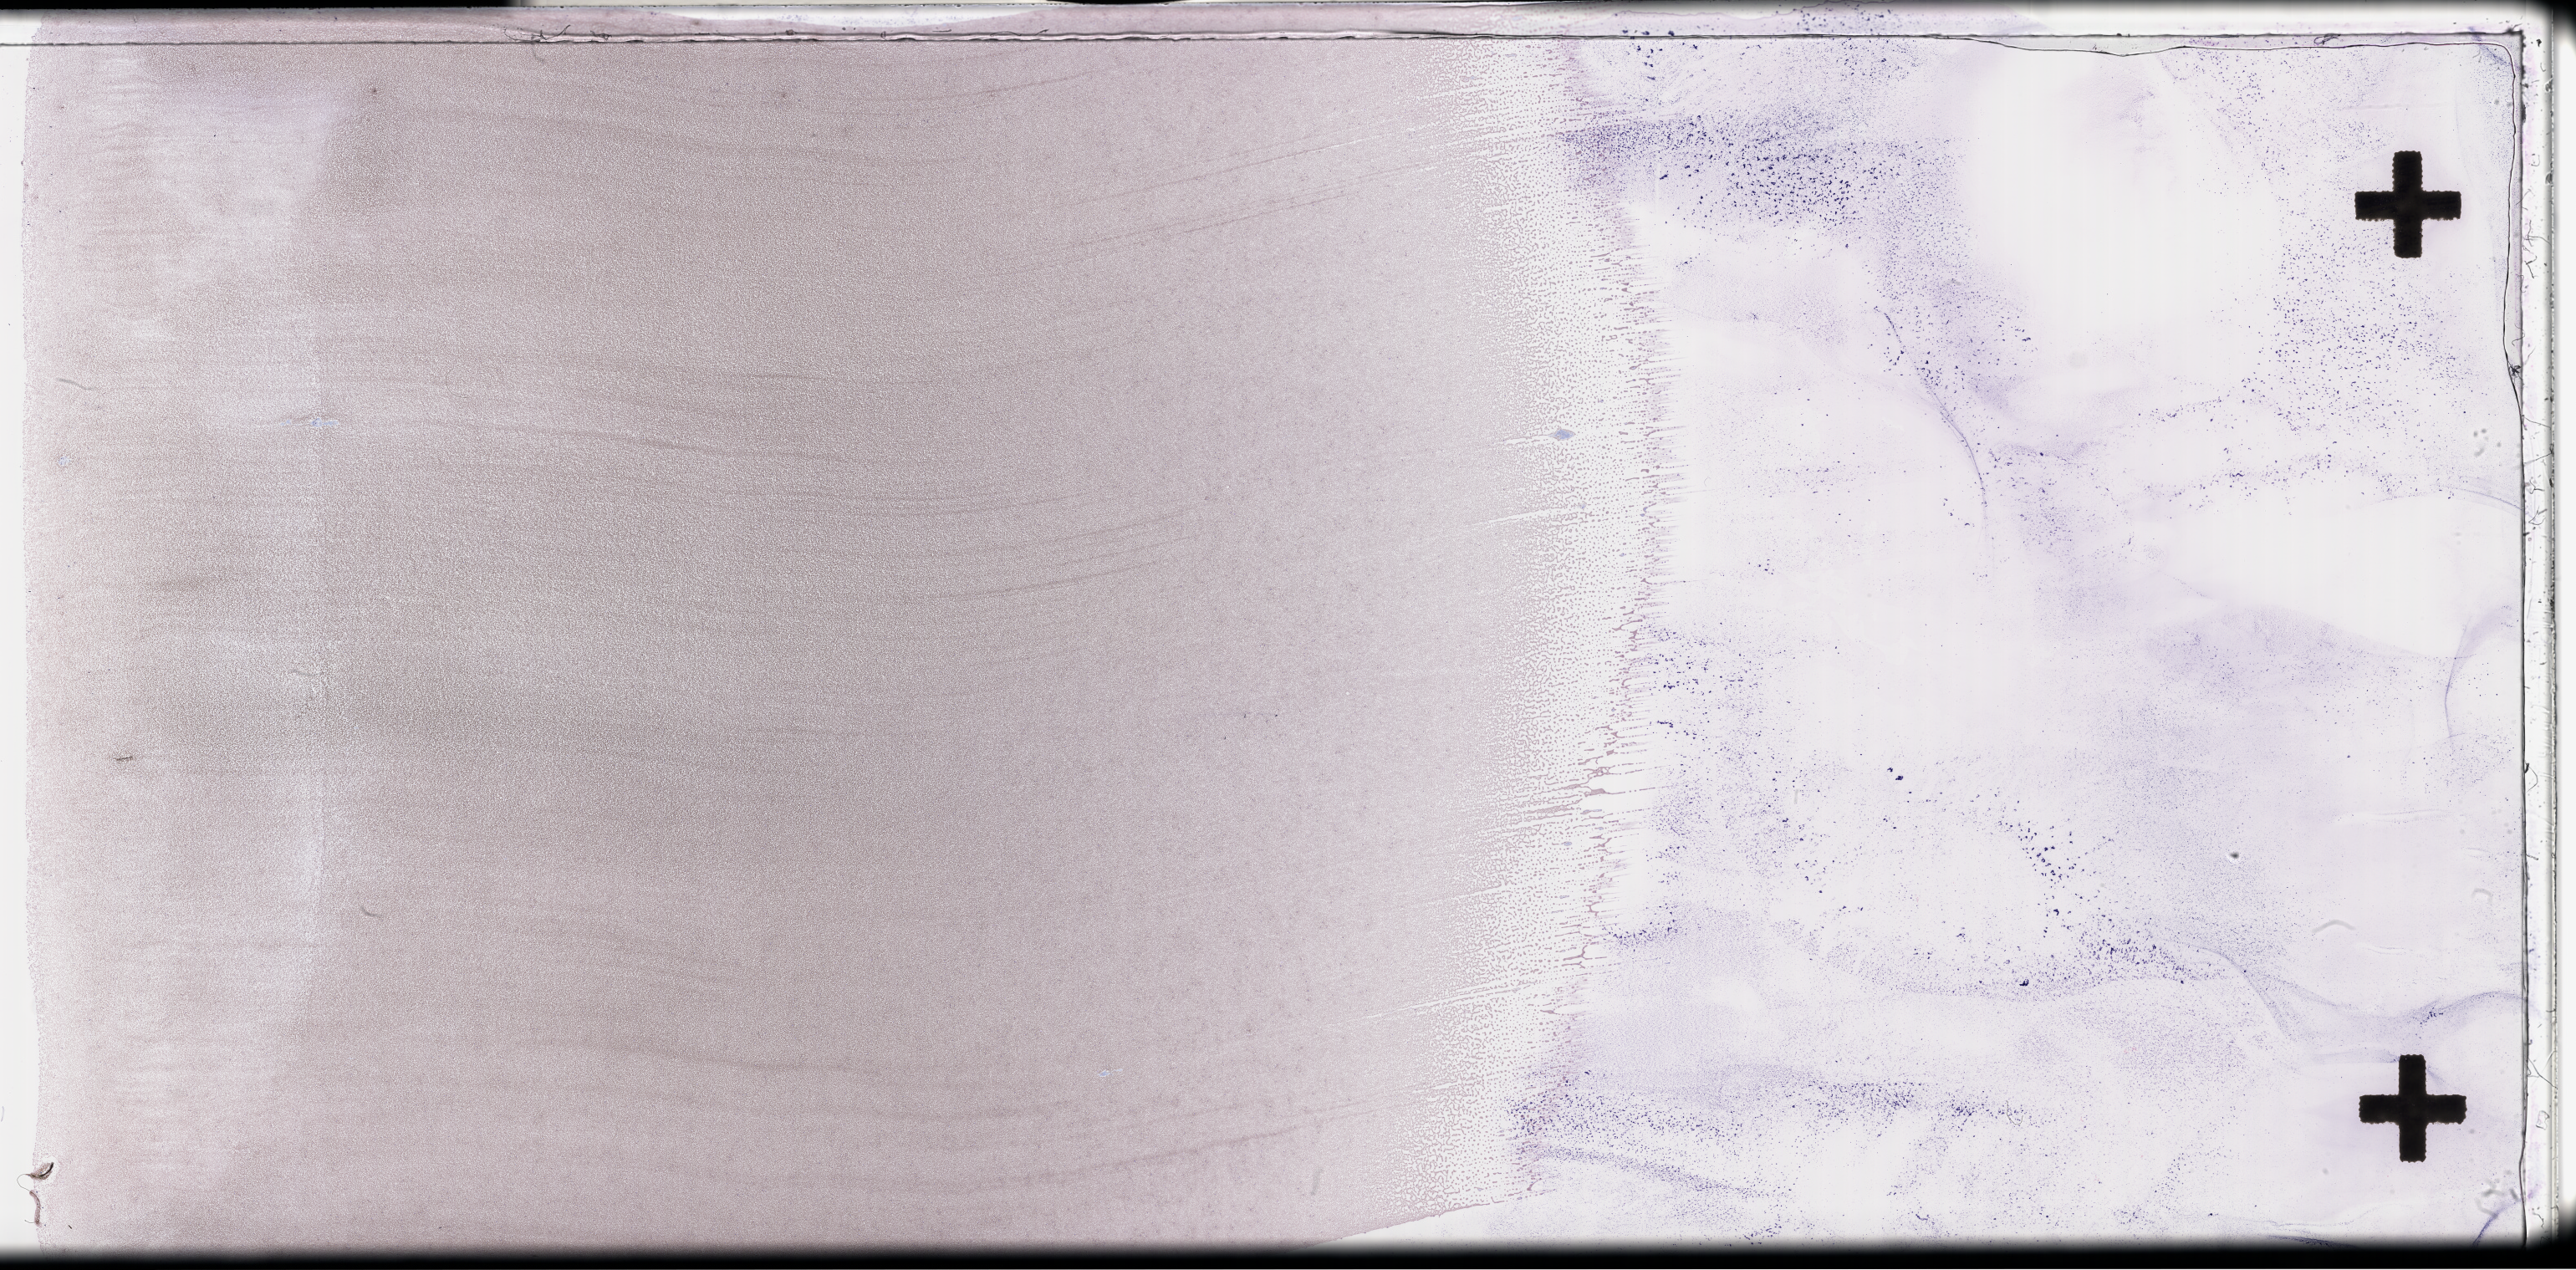
Wright–Giemsa-stained whole blood smear, whole-slide image — low-resolution overview of the scanned area, about 49.8 x 24.5 mm, smear from an EDTA sample. Patient: female.
• patient diagnosis: Plasma Cell Myeloma